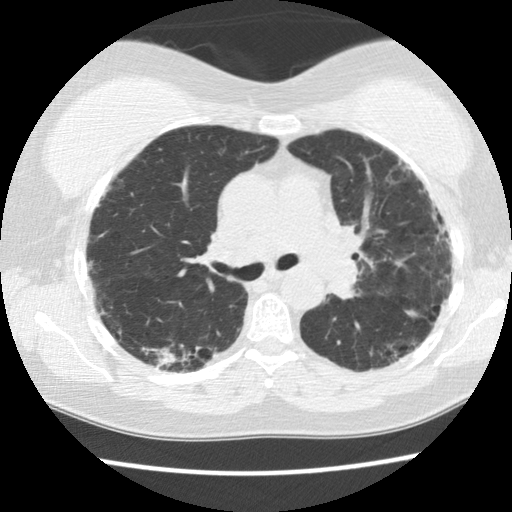
Low-dose screening chest CT, one axial slice; position 93 of 142 along the scan axis; 120 kVp; lung window (W 1500 / L -600 HU); 2.5 mm slice thickness; 512 × 512 image matrix.
Structures marked on this image (manually delineated by an expert):
- lesion 1 (tumor): bounding box [x1, y1, x2, y2] px = [406, 311, 415, 315]